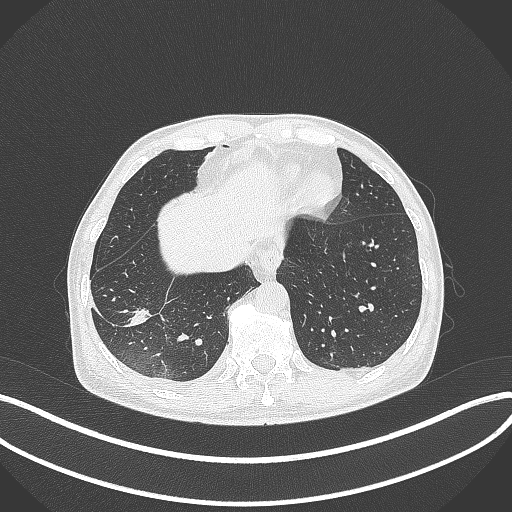
Chest CT, one axial slice. Slice 84 of 388 in the series (ordered by position). Lung window (W 1500 / L -600 HU). 1 mm slice thickness. 512 × 512 image matrix. Male patient, age 64 years. Case-level facts recorded for this patient, not image findings: clinical TNM (as recorded): T3 N0 M0; histopathological grade: G2-3.
Outlined on this slice (bounding box drawn by a radiologist):
- lung tumour (recorded histology: adenocarcinoma): bounding box (x1, y1, x2, y2) in pixels: (123, 307, 150, 332)